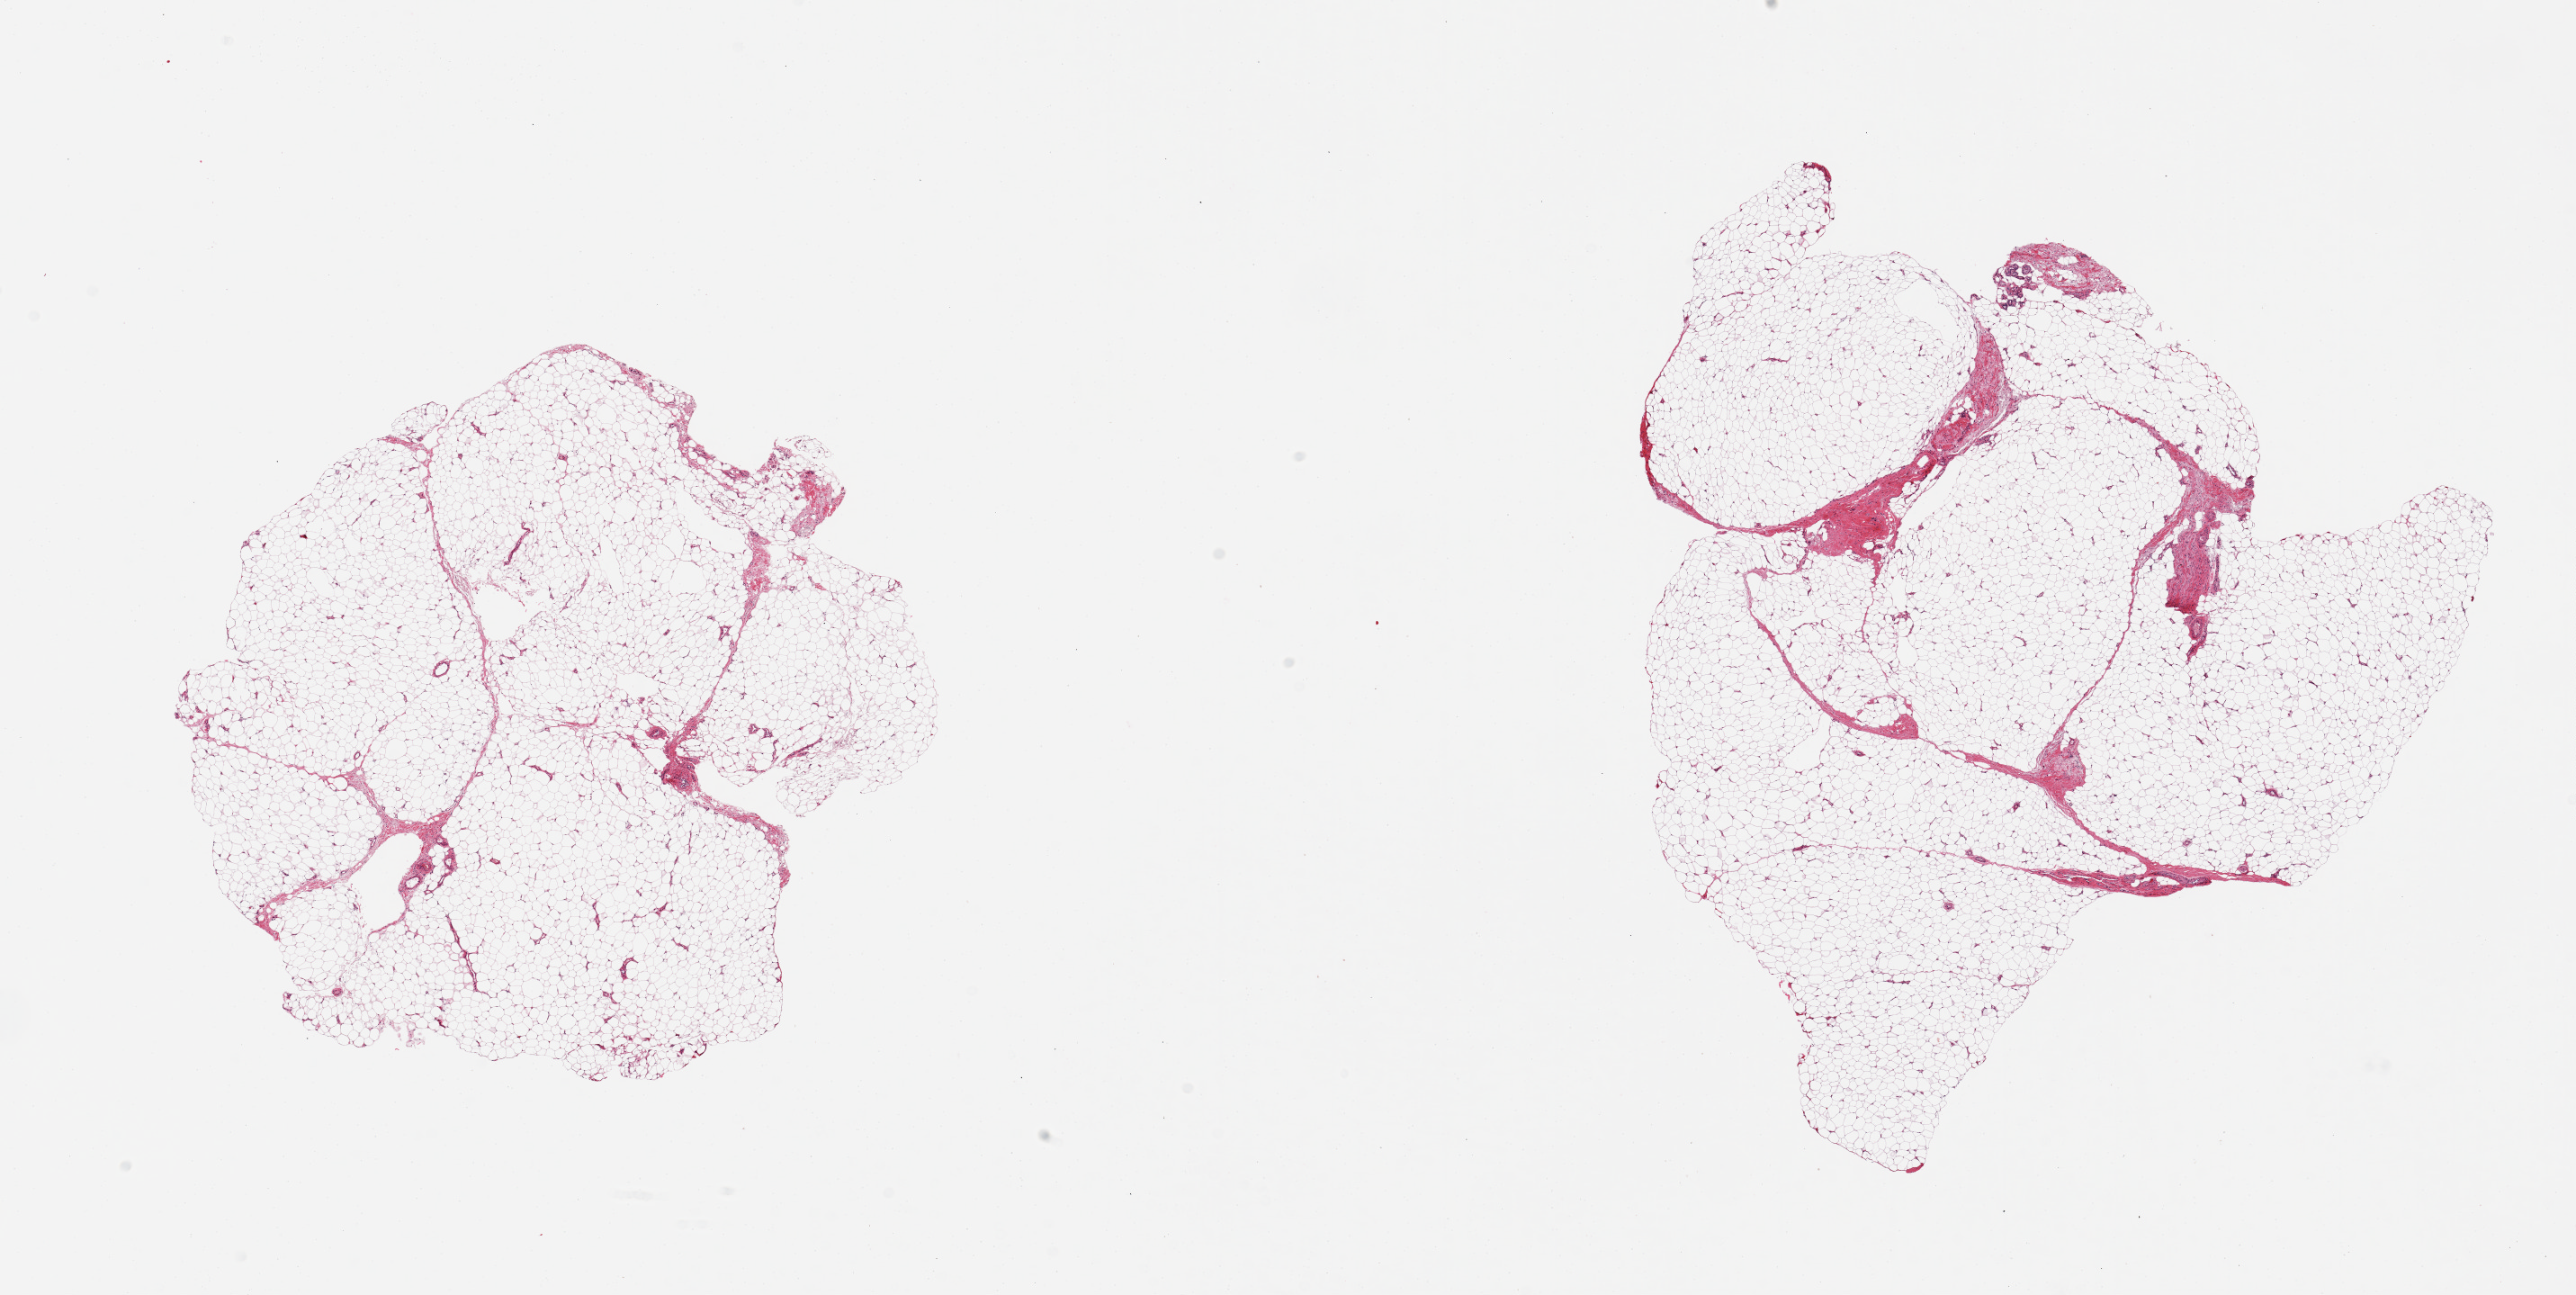
Hematoxylin and eosin (H&E) whole-slide image — a low-resolution overview of the entire scanned area, about 22.6 x 11.4 mm. PAXgene-fixed, paraffin-embedded tissue. Target tissue: adipose tissue. Donor tissue sample. Female donor.
Review note (as recorded): 2 pieces; 5% fibrous content.